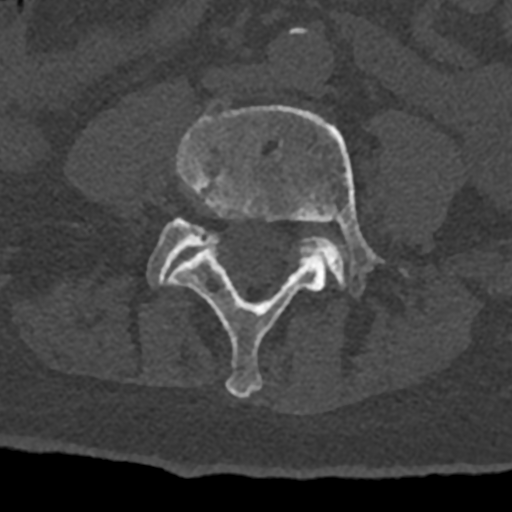
CT including the spine, one axial slice. Position 243 of 797 along the scan axis. Bone window (W 1800 / L 400 HU). 0.5 mm slice thickness. 512 × 512 image matrix. Male patient, age 74 years. Case-level facts recorded for this patient, not image findings: primary cancer: renal; vertebrae with lytic lesions (as recorded): T10, L1, L2, L3, L4, L5.
Outlined on this slice (semi-automatically segmented with operator editing):
- L4 vertebra: box from (x=167, y=105) to (x=405, y=398) px
- L5 vertebra: (x=147, y=217)–(x=345, y=287)